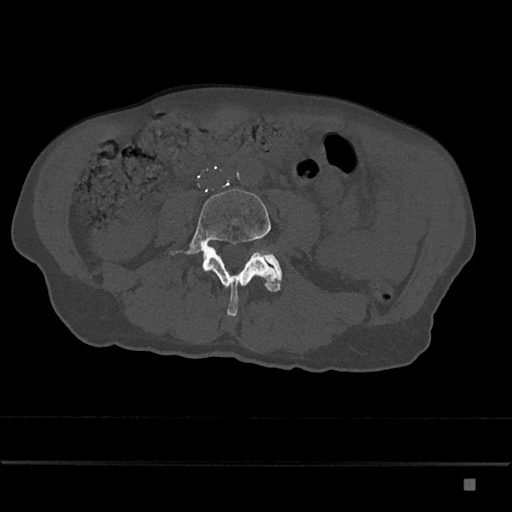
CT including the spine, one axial slice. Position 332 of 797 along the scan axis. Reconstruction kernel Br40s/3. 120 kVp. Bone window (W 1800 / L 400 HU). 0.5 mm slice thickness. 512 × 512 image matrix. Male patient, age 72 years. Case-level facts recorded for this patient, not image findings: primary cancer: prostate.
Outlined on this slice (semi-automatic segmentation, software-assisted and operator-edited):
- L4 vertebra: bounding box <169,189,281,317> (left, top, right, bottom; pixels)
- L5 vertebra: <266,255,282,280>